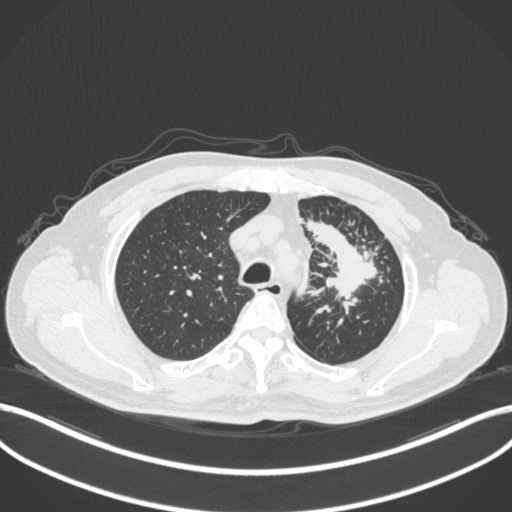
Chest CT, one axial slice. Slice 277 of 386 in the series (ordered by position). Reconstruction kernel B31f. 120 kVp. Lung window (W 1500 / L -600 HU). 1 mm slice thickness. 512 × 512 image matrix, field of view 400 × 400 mm. Male patient, age 69 years. From the clinical record (not read from this slice): clinical TNM (as recorded): T2a N2 M0.
Structures marked on this image (bounding box drawn by a radiologist):
- lung tumour (recorded histology: adenocarcinoma): bounding box [x1, y1, x2, y2] px = [304, 214, 377, 302]